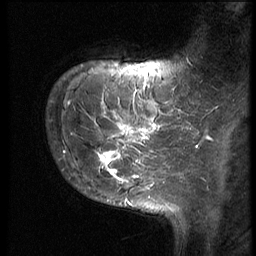
Breast MRI (dynamic contrast-enhanced), one sagittal slice; position 10 of 62 along the scan axis; 3 images stored at this slice position (order not interpretable as contrast timing); 1.5 T; TE 4.2 ms, TR 9 ms; 2.5 mm slice thickness; 256 × 256 image matrix, field of view 180 × 180 mm. Female patient, age 28 years. Case-level facts recorded for this patient, not image findings: setting: breast cancer imaged before/during neoadjuvant chemotherapy.
Annotated regions visible in this slice (semi-automatically segmented with operator editing):
- analysis volume of interest (the breast-tissue region the enhancement analysis was run in; not a lesion): box from (x=46, y=81) to (x=192, y=187) px
- tumour enhancement mask (voxels above the 140 % enhancement threshold inside the analysis volume of interest): (x=63, y=90)–(x=192, y=183)